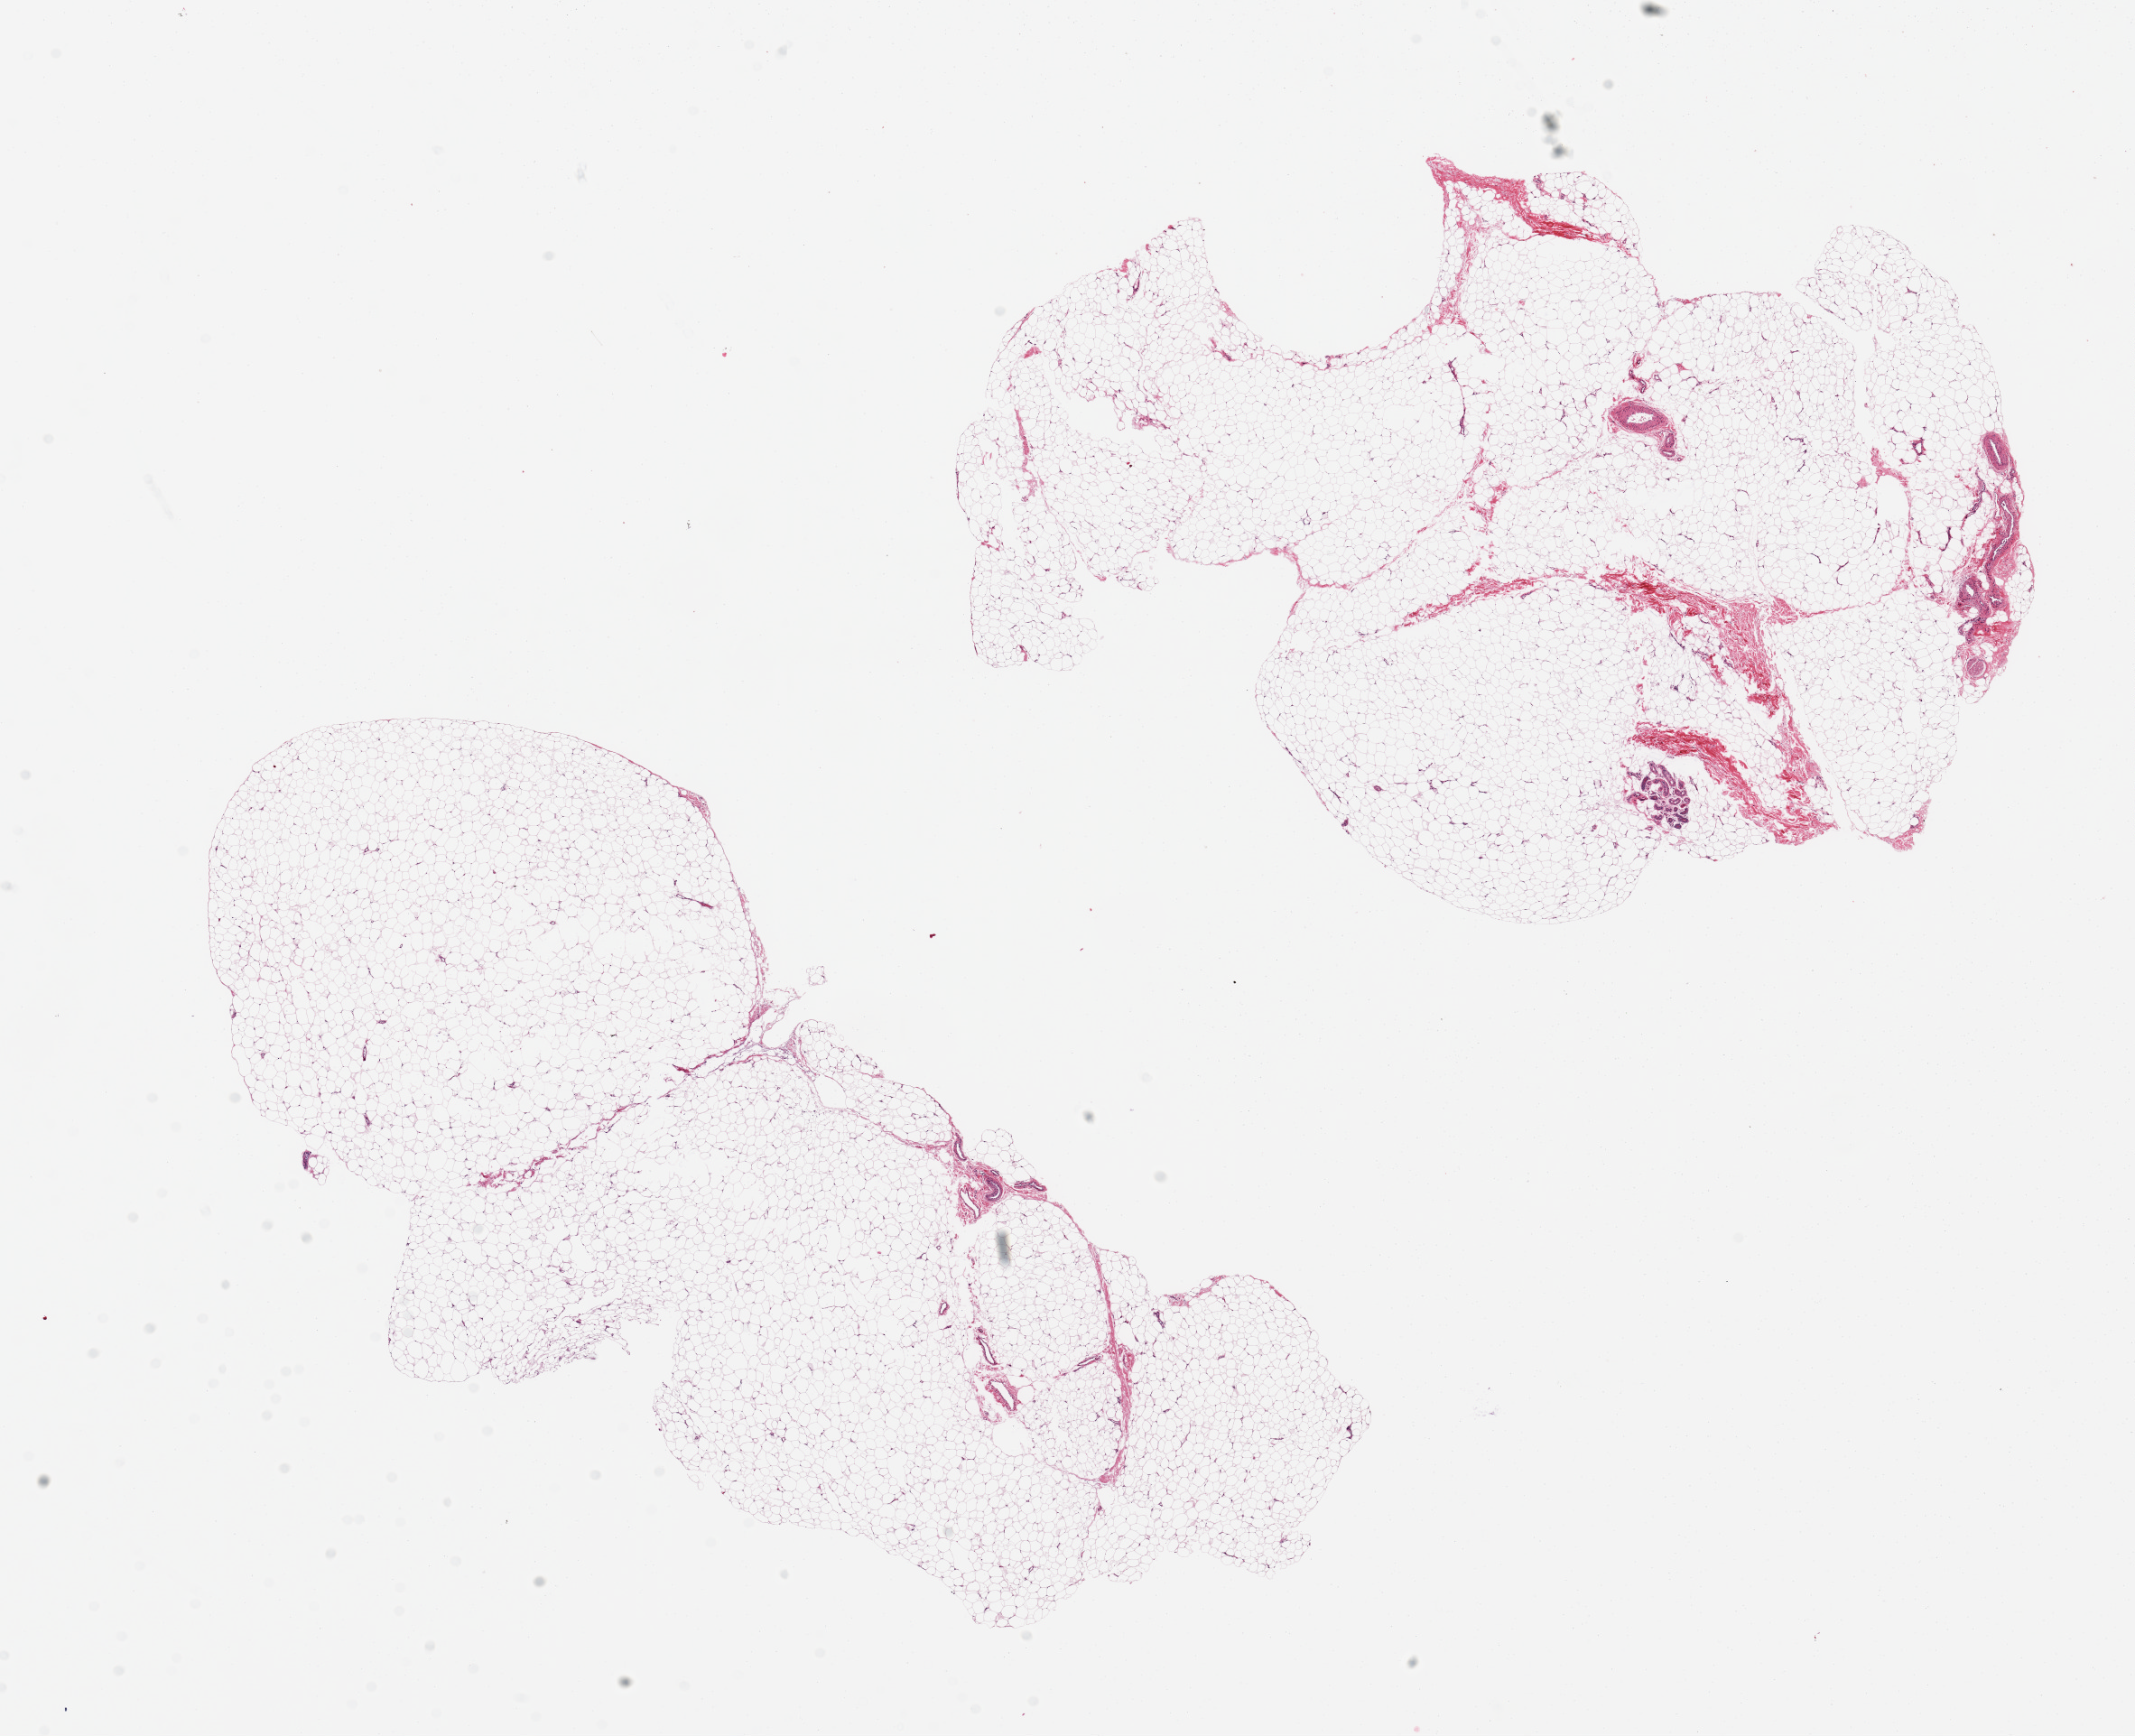
Haematoxylin and eosin whole-slide image — low-resolution overview of the scanned area, about 18.7 x 15.2 mm (slide scanned at 20x). PAXgene-fixed paraffin-embedded (PFPE) section. Sampled site (target tissue): adipose tissue. Tissue donor sample.
• pathologist's review note for this sample: 2 pieces~10x4mm,9x6mm; small sweat gland